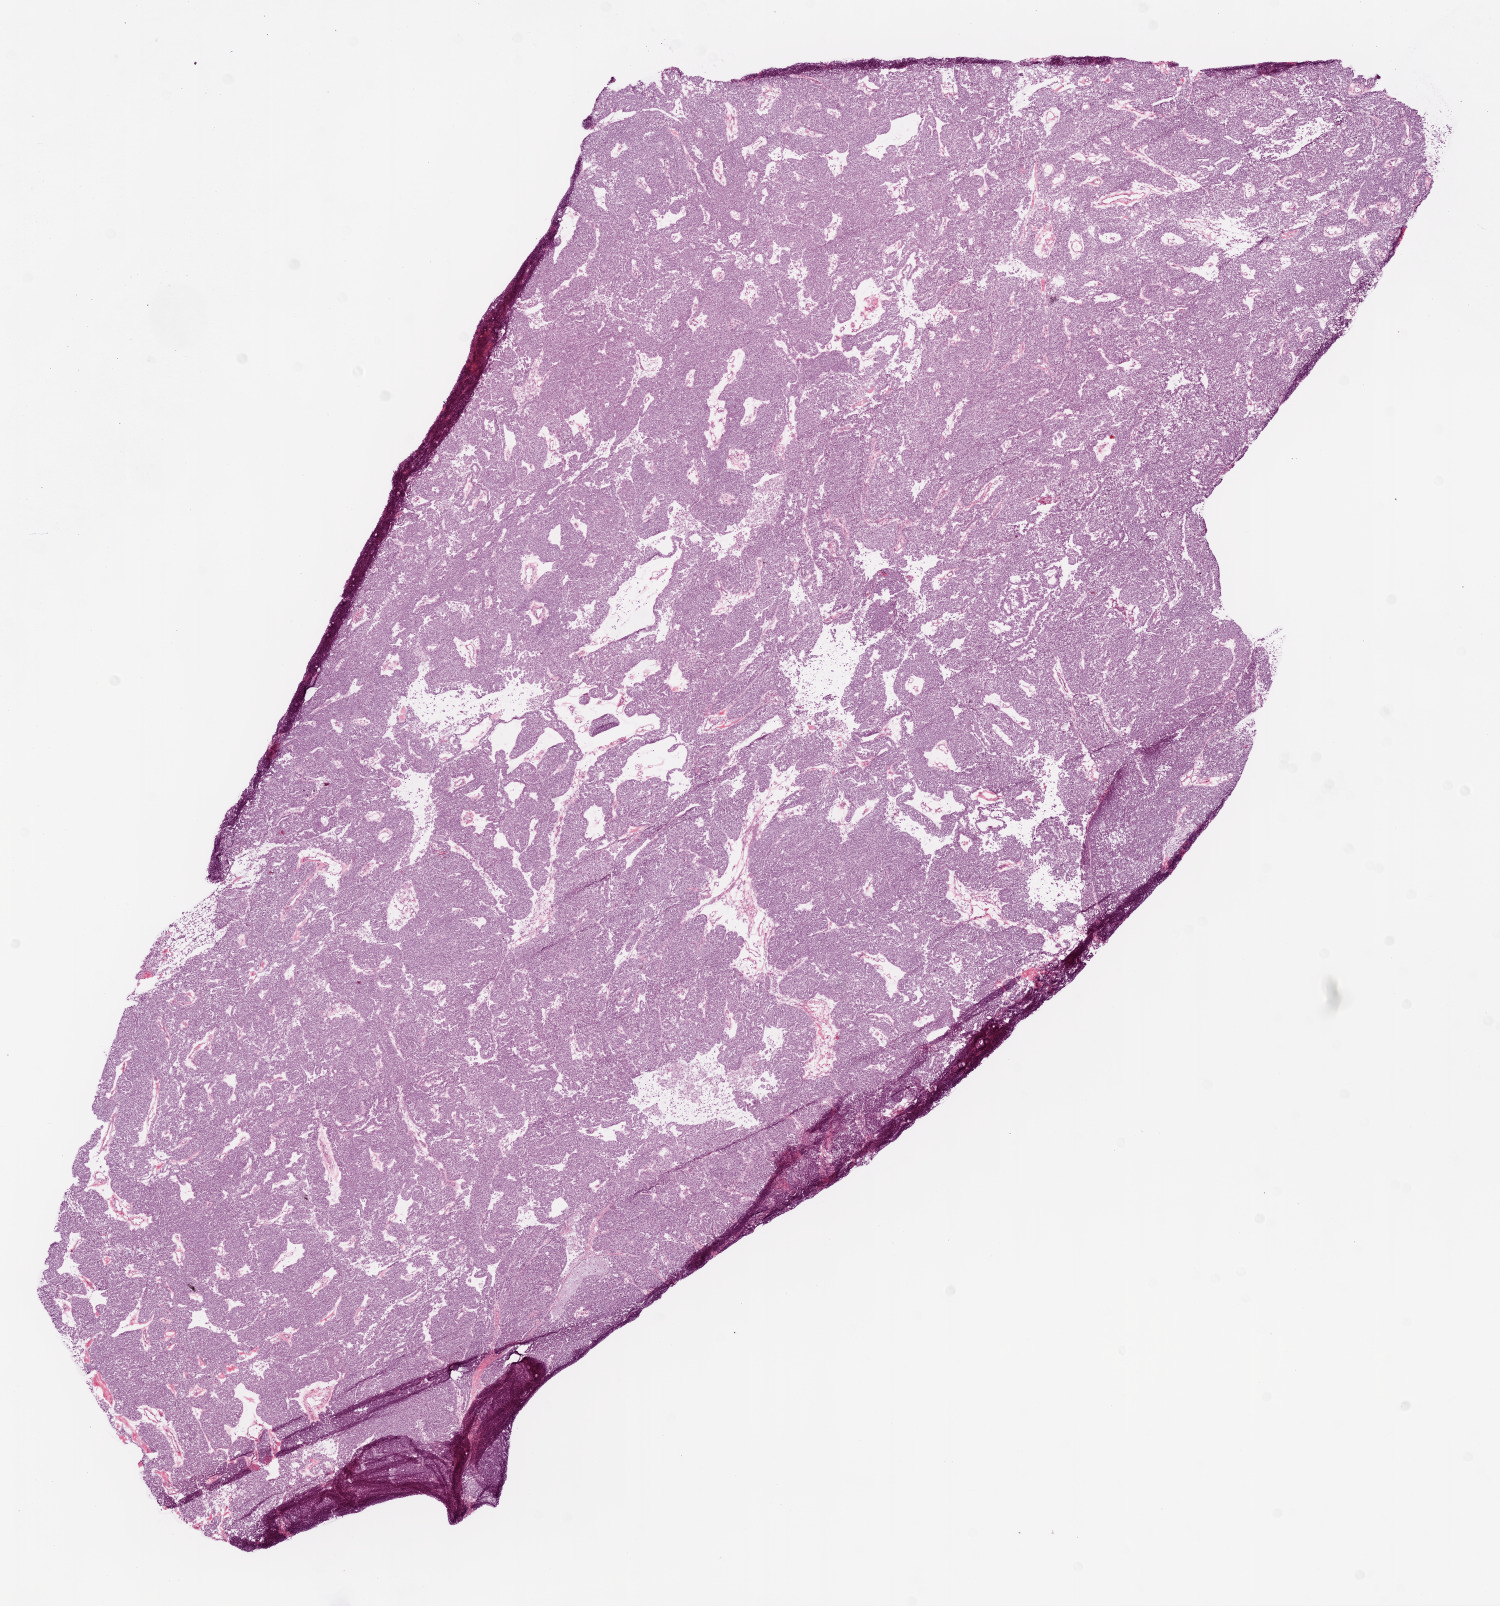
Hematoxylin and eosin (H&E) stained whole-slide image — a low-resolution overview of the entire scanned area, about 12.0 x 12.9 mm (acquisition: 20x scan); frozen section from the bottom of the tissue portion; primary tumour sample from the ovary. Patient: female, age at initial diagnosis 57 years. Histologic grade: G3 (poorly differentiated). Slide review estimates, as recorded: tumour cells 93%, tumour nuclei 95%, normal cells 0%, stromal cells 5%, necrosis 2%.
- FIGO stage: IIIC
- diagnosis: Serous cystadenocarcinoma, NOS